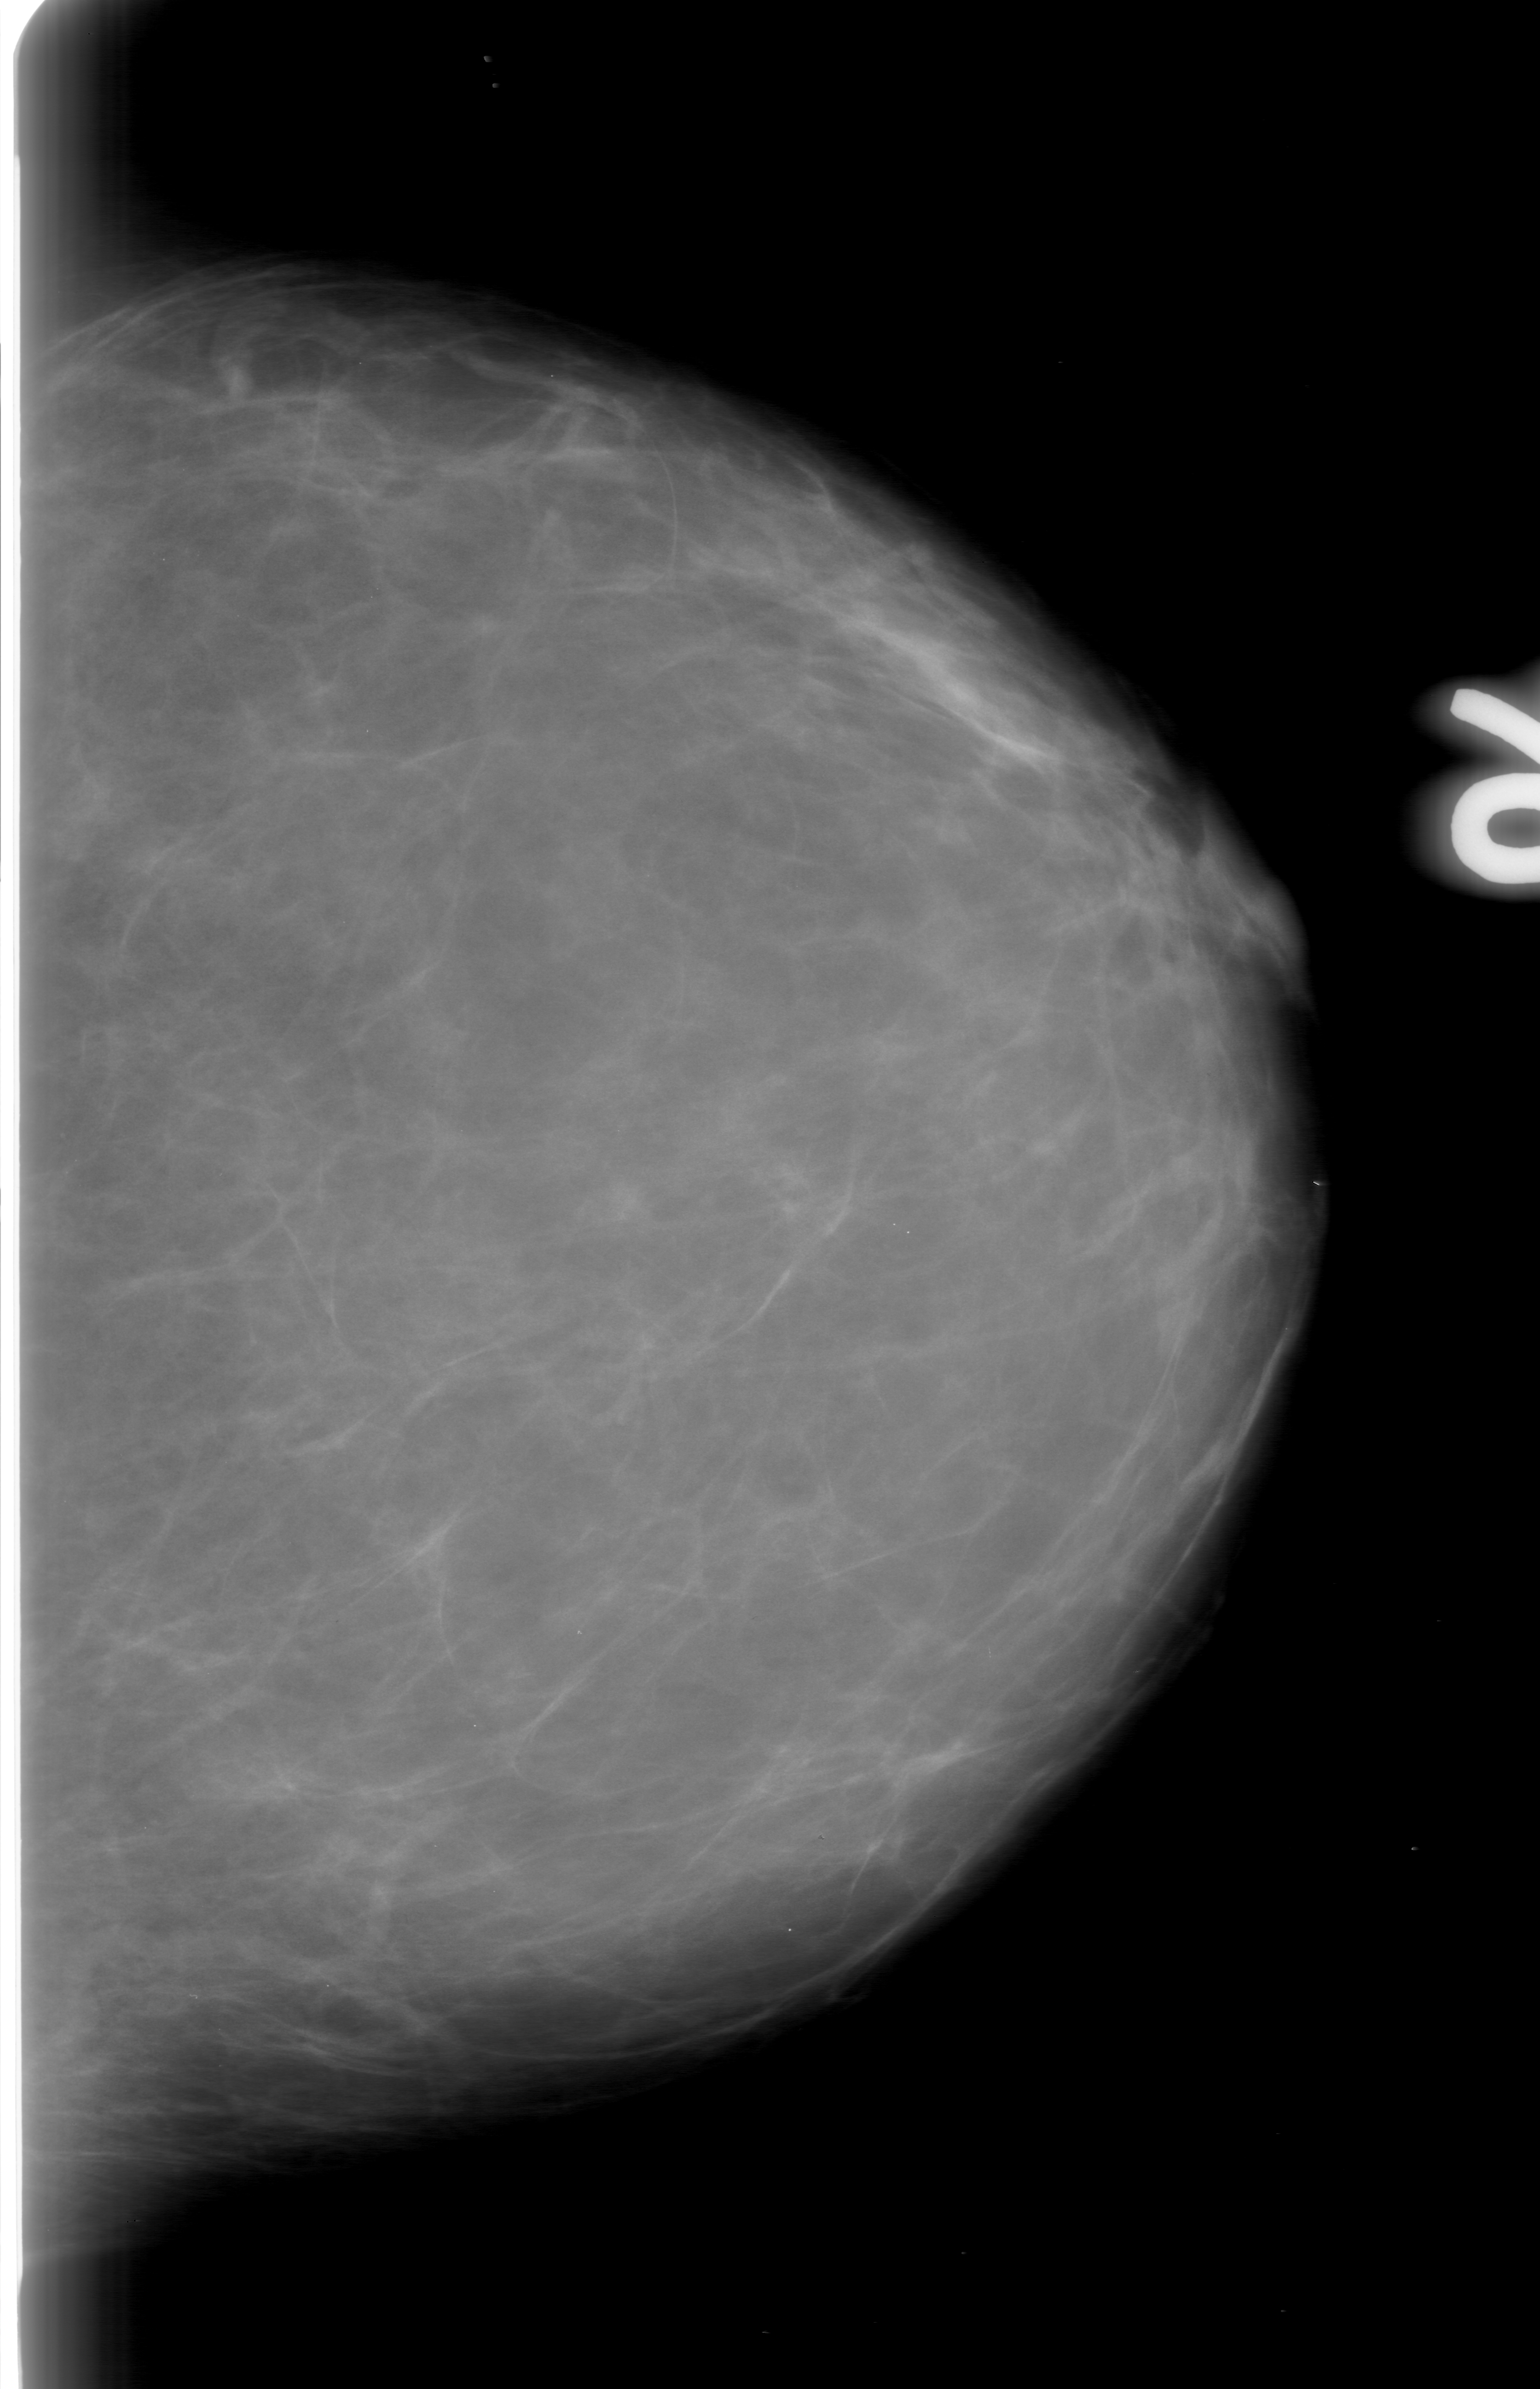
Digitized screen-film mammogram, left breast, craniocaudal (CC) view, BI-RADS breast density category 1 (scale 1–4).
- Radiologist-marked abnormalities on this image: mass, shape irregular, margins obscured; BI-RADS assessment category 0 (incomplete: needs additional imaging); subtlety rating 4 on a 1 (subtle) to 5 (obvious) scale; pathology (as recorded): benign.